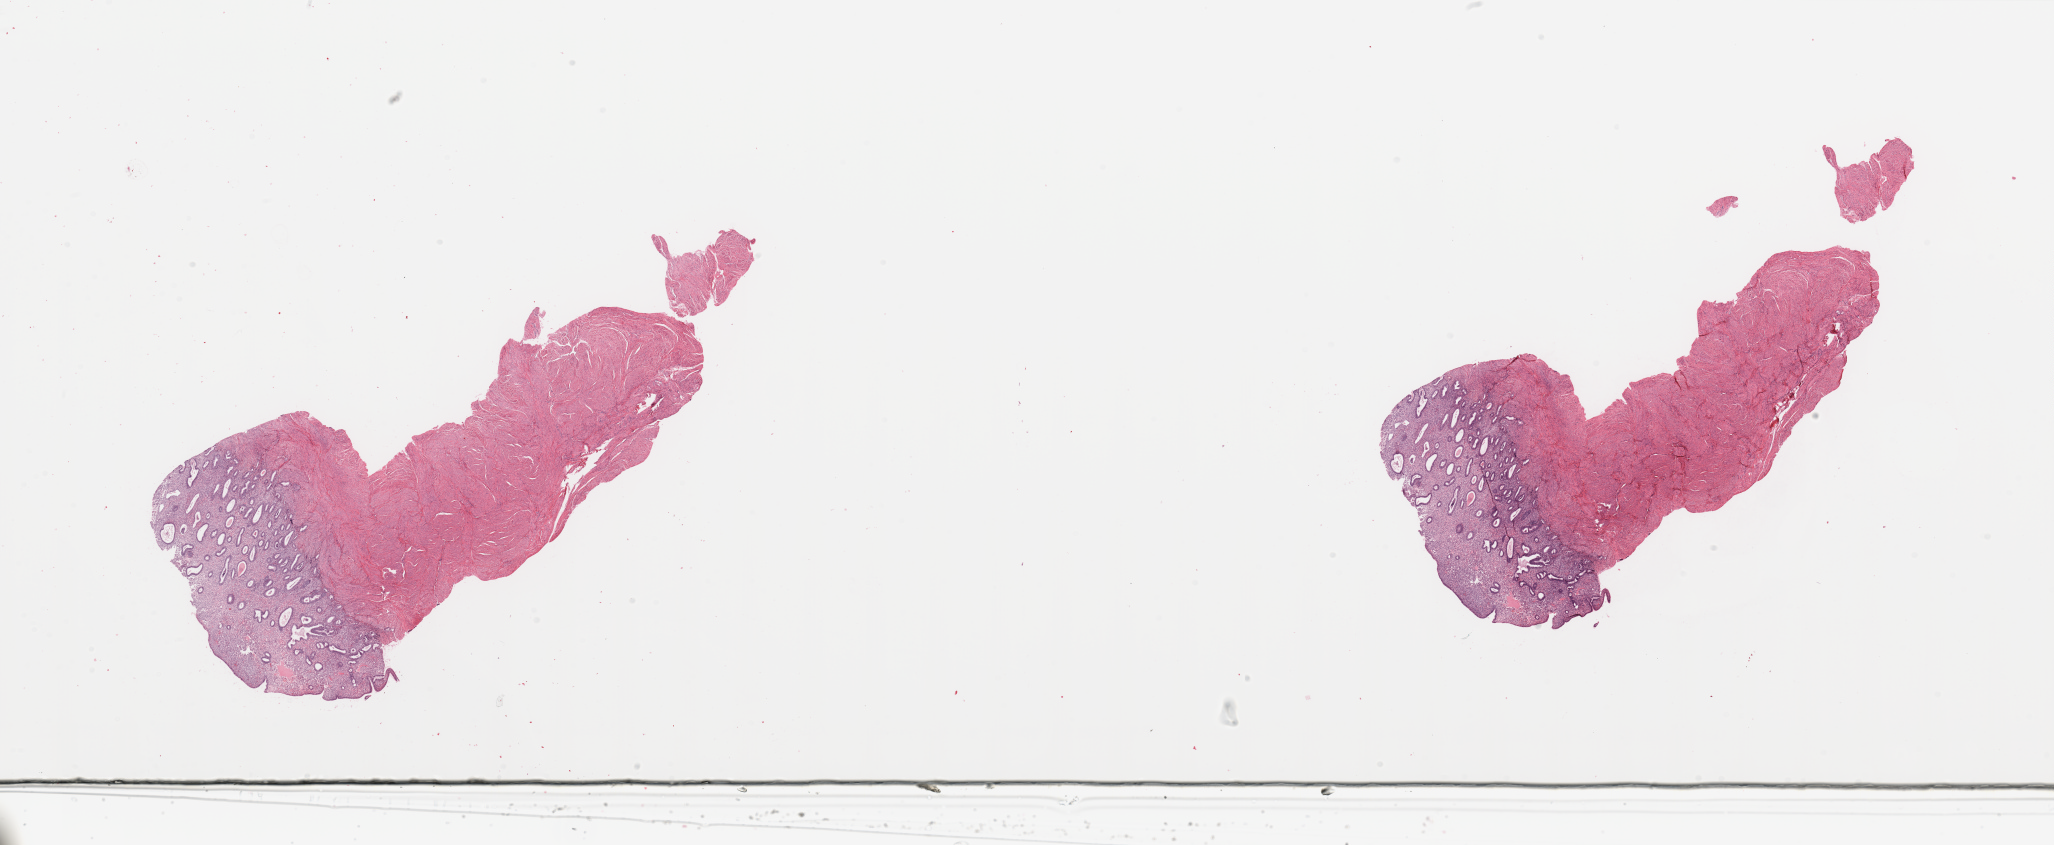
Digitized H&E tissue section (whole slide), shown as a low-resolution overview of the whole scanned area (about 32.5 x 13.4 mm); normal (non-tumour) tissue sample, sampled site: uterus. 51-year-old female patient.
This section: normal (non-tumour) tissue from the same patient. Patient diagnosis: Endometrioid adenocarcinoma, NOS.